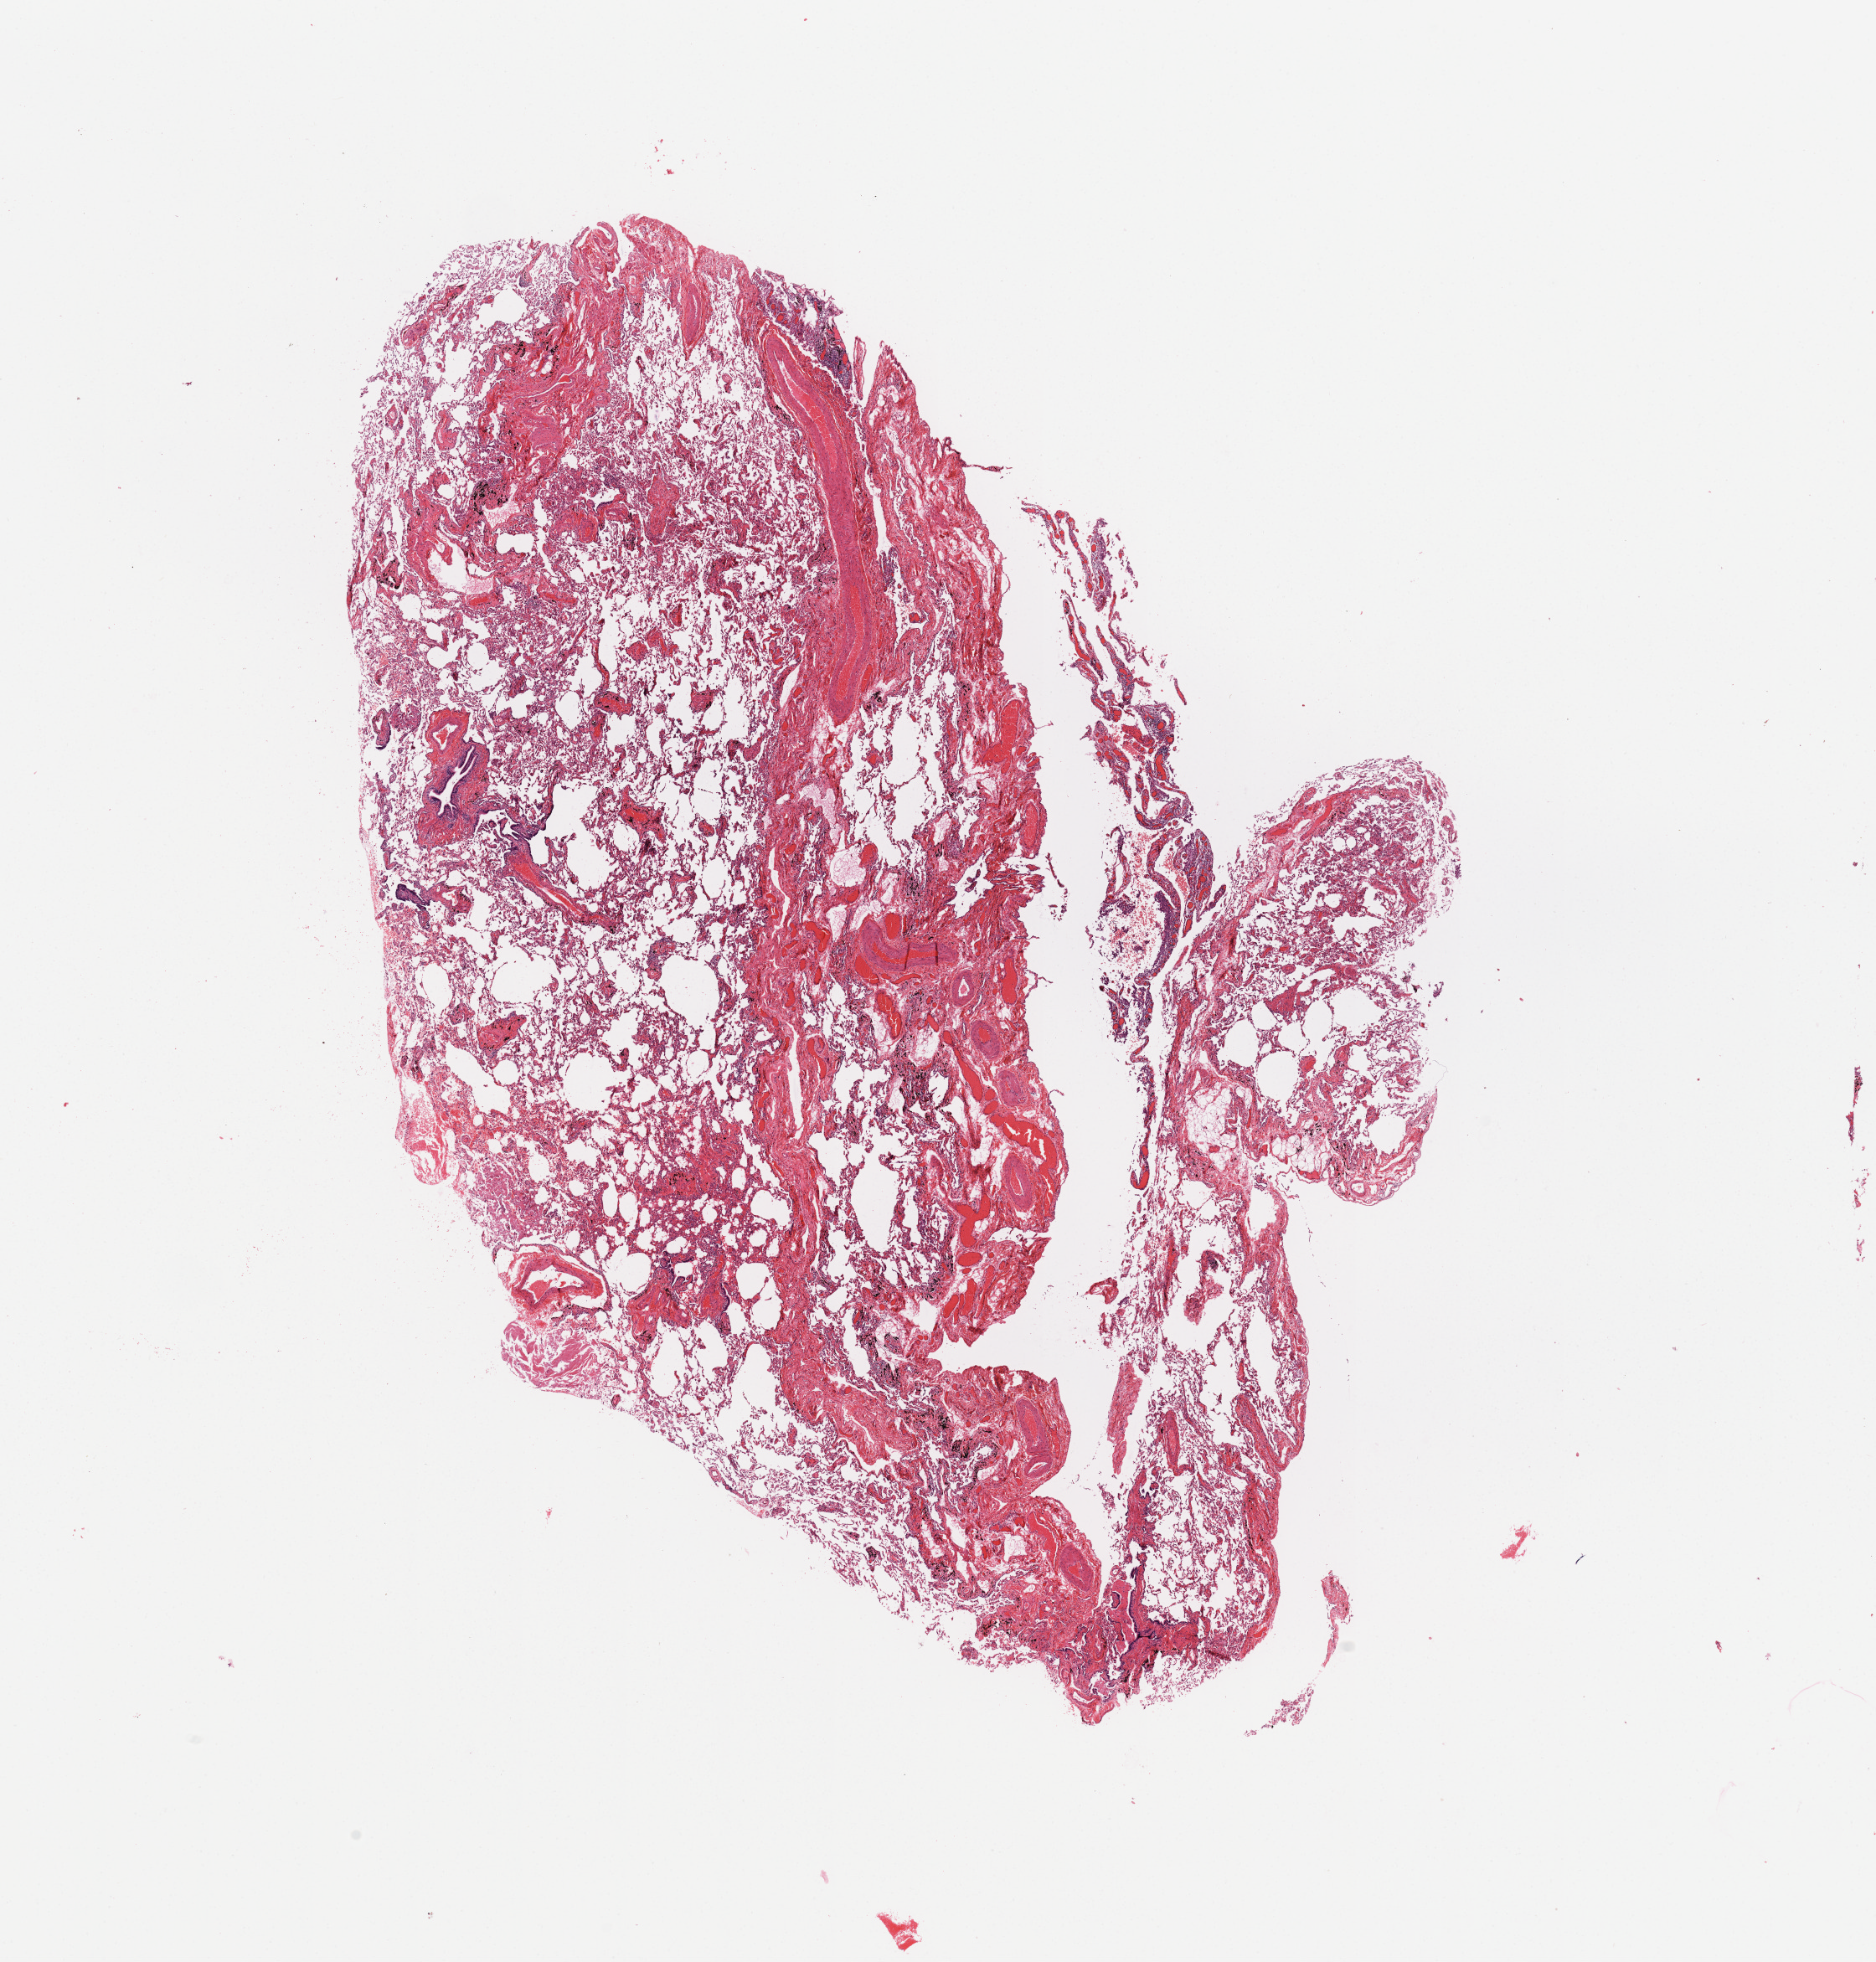
Digitized H&E tissue section (whole slide), a low-resolution overview of the entire scanned area, about 17.7 x 18.5 mm, normal (non-tumour) tissue sample, sampled site: lung. Male, 67 y/o.
This section: normal (non-tumour) tissue from the same patient. Patient diagnosis: Squamous cell carcinoma, NOS.